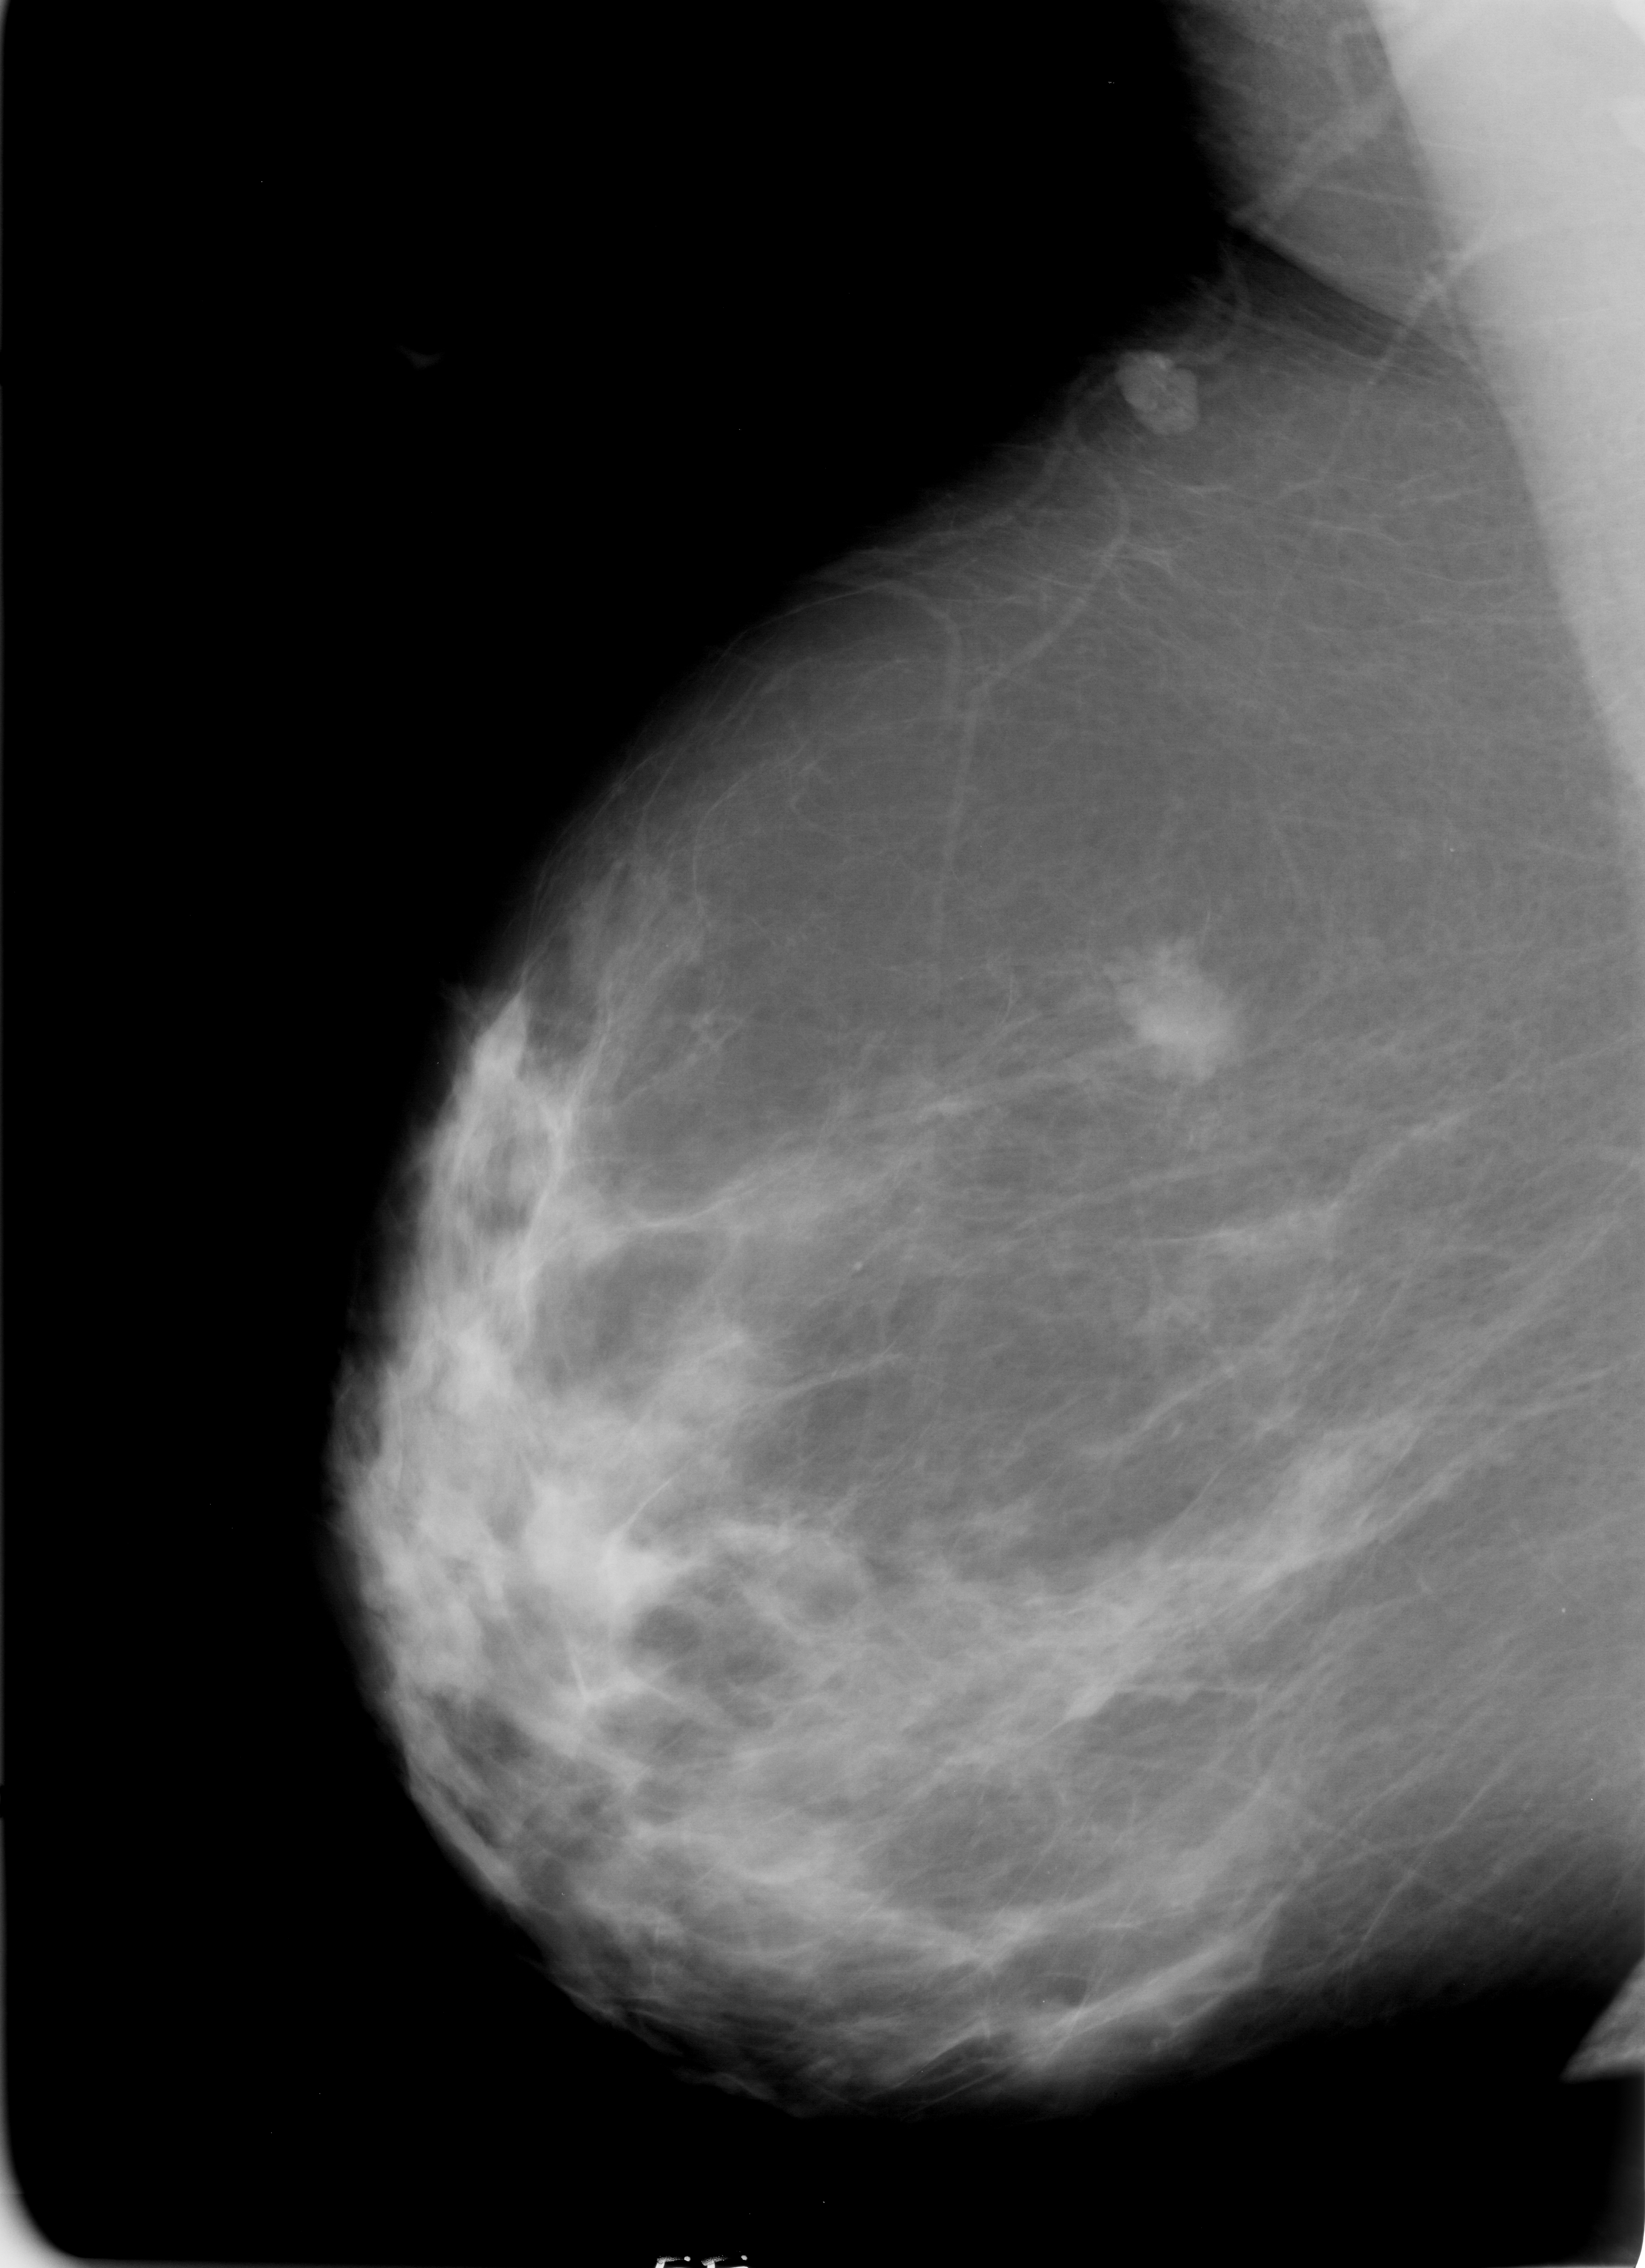
Digitized screen-film mammogram; right breast; mediolateral oblique (MLO) view; breast composition: scattered fibroglandular densities (BI-RADS density category 2 of 4); 1645 × 2268 image matrix.
Expert-marked regions of interest on this image (one box per marked abnormality):
- mass, shape lobulated, margins circumscribed / ill defined; BI-RADS assessment category 4; subtlety rating 4 on a 1 (subtle) to 5 (obvious) scale; pathology result (as recorded, not read from the image): malignant: bounding box (x1, y1, x2, y2) in pixels: (1113, 944, 1234, 1071)